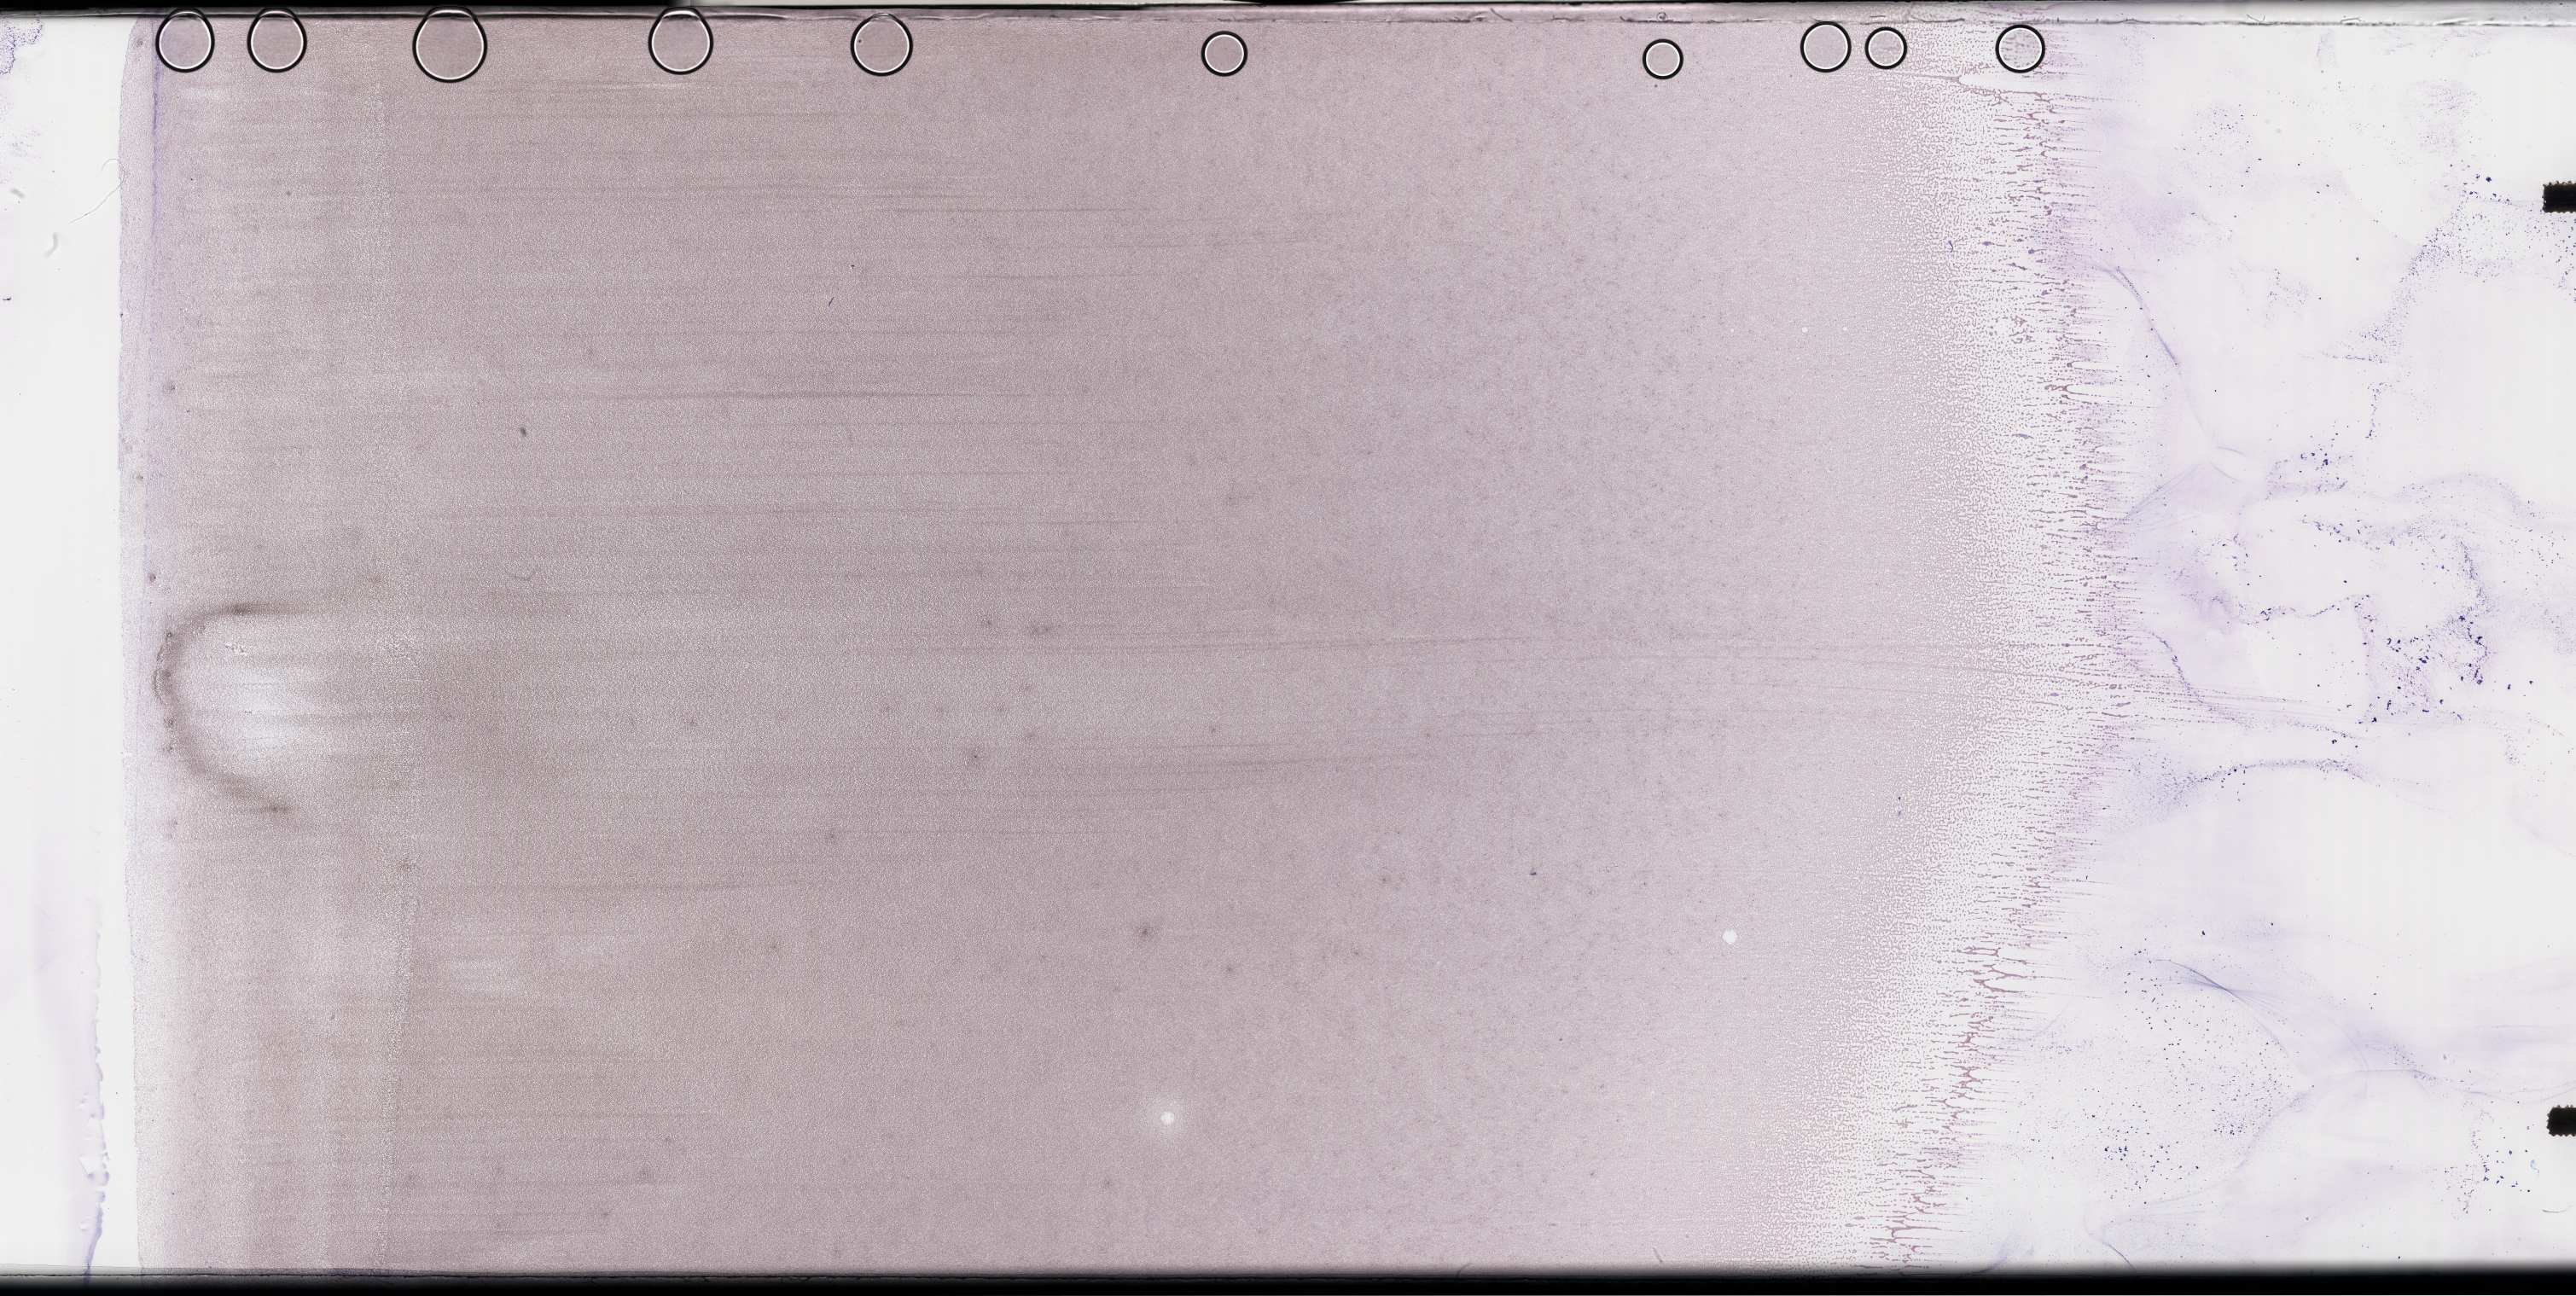
Whole-slide image of a whole blood smear, Wright-Giemsa stain, whole scanned area (about 48.8 x 24.5 mm) shown as a low-resolution overview. Patient sex: male.
* from a patient with: Plasma Cell Myeloma